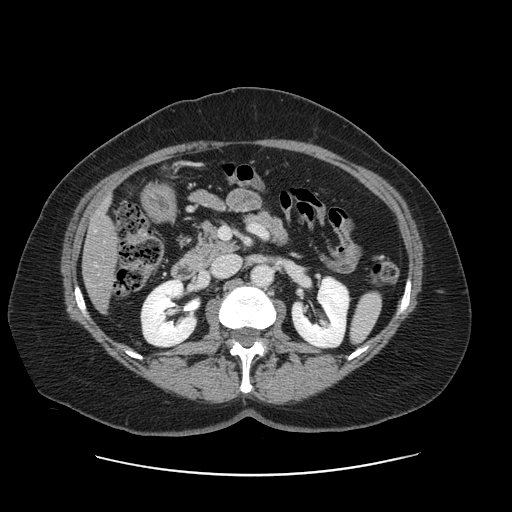
Contrast-enhanced abdominal CT, one axial slice; 120 kVp; soft-tissue window (W 400 / L 40 HU); 512 × 512 image matrix. Female patient, age 62 years. Case-level facts recorded for this patient, not image findings: diagnosis: colorectal cancer liver metastases, imaged before liver resection; multiple liver metastases: no; largest metastasis: 2.5 cm; disease in both lobes: no.
Outlined on this slice (manually delineated by an expert):
- liver: bounding box <84,205,116,309> (left, top, right, bottom; pixels)